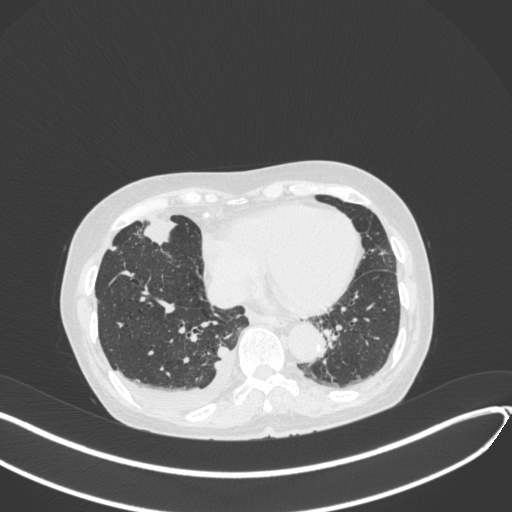
Chest CT, one axial slice. Reconstruction kernel B31f. Lung window (W 1500 / L -600 HU). 512 × 512 image matrix, field of view 400 × 400 mm. Patient: female, 75 years. From the clinical record (not read from this slice): clinical TNM (as recorded): T2a N3 M0.
Outlined on this slice (bounding box drawn by a radiologist):
- lung tumour (recorded histology: adenocarcinoma): bounding box (x1, y1, x2, y2) in pixels: (140, 214, 179, 246)